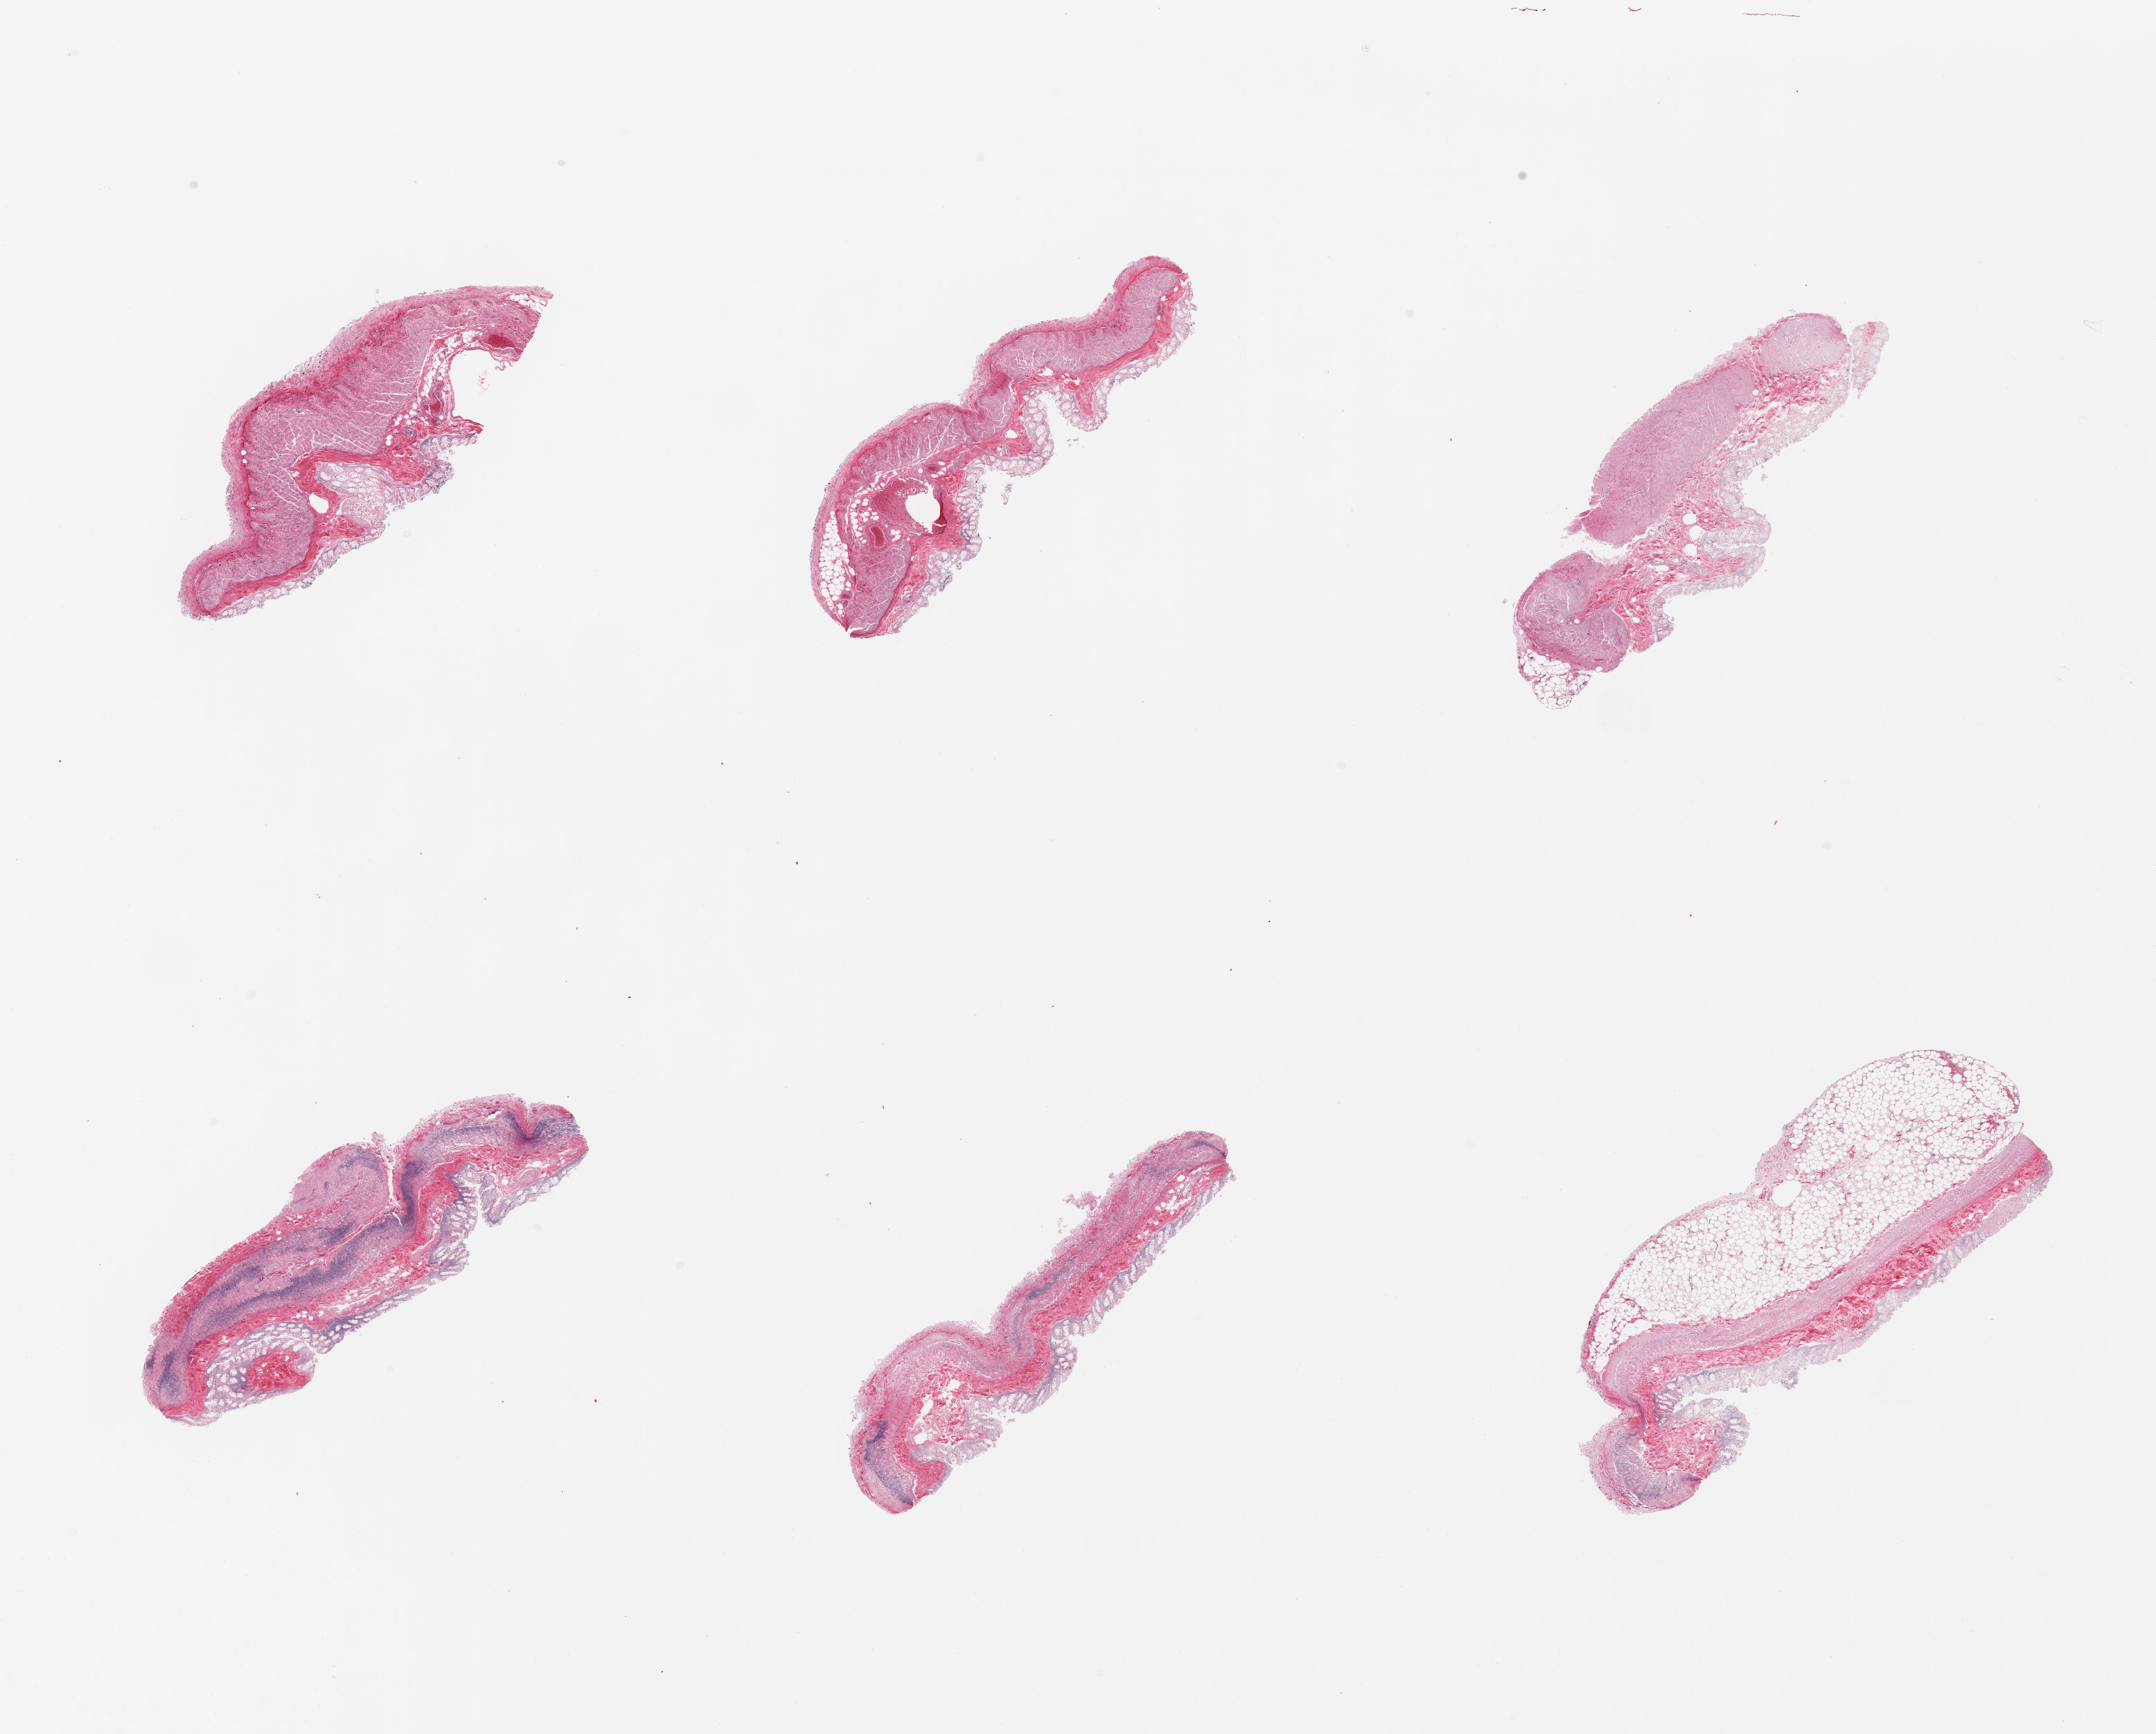
Digitized H&E-stained section, brightfield — low-resolution overview of the scanned area, about 24.6 x 19.8 mm (acquisition: 20x scan). PAXgene-fixed, paraffin-embedded tissue. Target tissue: transverse colon. Donor tissue sample. Donor sex: female.
- pathologist's review note for this sample: 6 pieces; full thickness sections, extensive autolysis